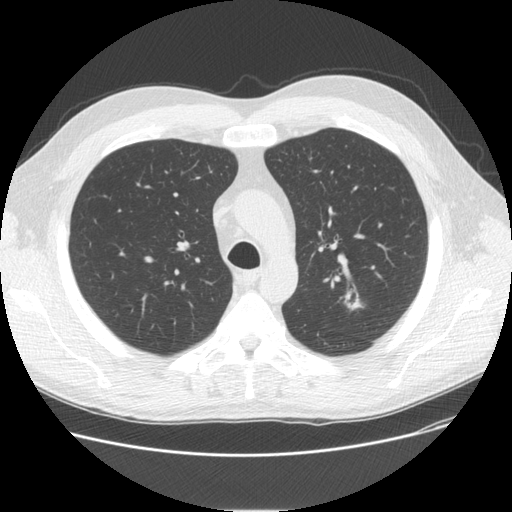
Low-dose screening chest CT, one axial slice. Slice 113 of 150 in the series (ordered by position). Reconstruction kernel STANDARD. Lung window (W 1500 / L -600 HU). 2.5 mm slice thickness. 512 × 512 image matrix, field of view 370 × 370 mm.
Structures marked on this image (manually delineated by an expert):
- lesion 1 (tumor, upper lobe of left lung): bounding box (x1, y1, x2, y2) in pixels: (345, 292, 362, 310)